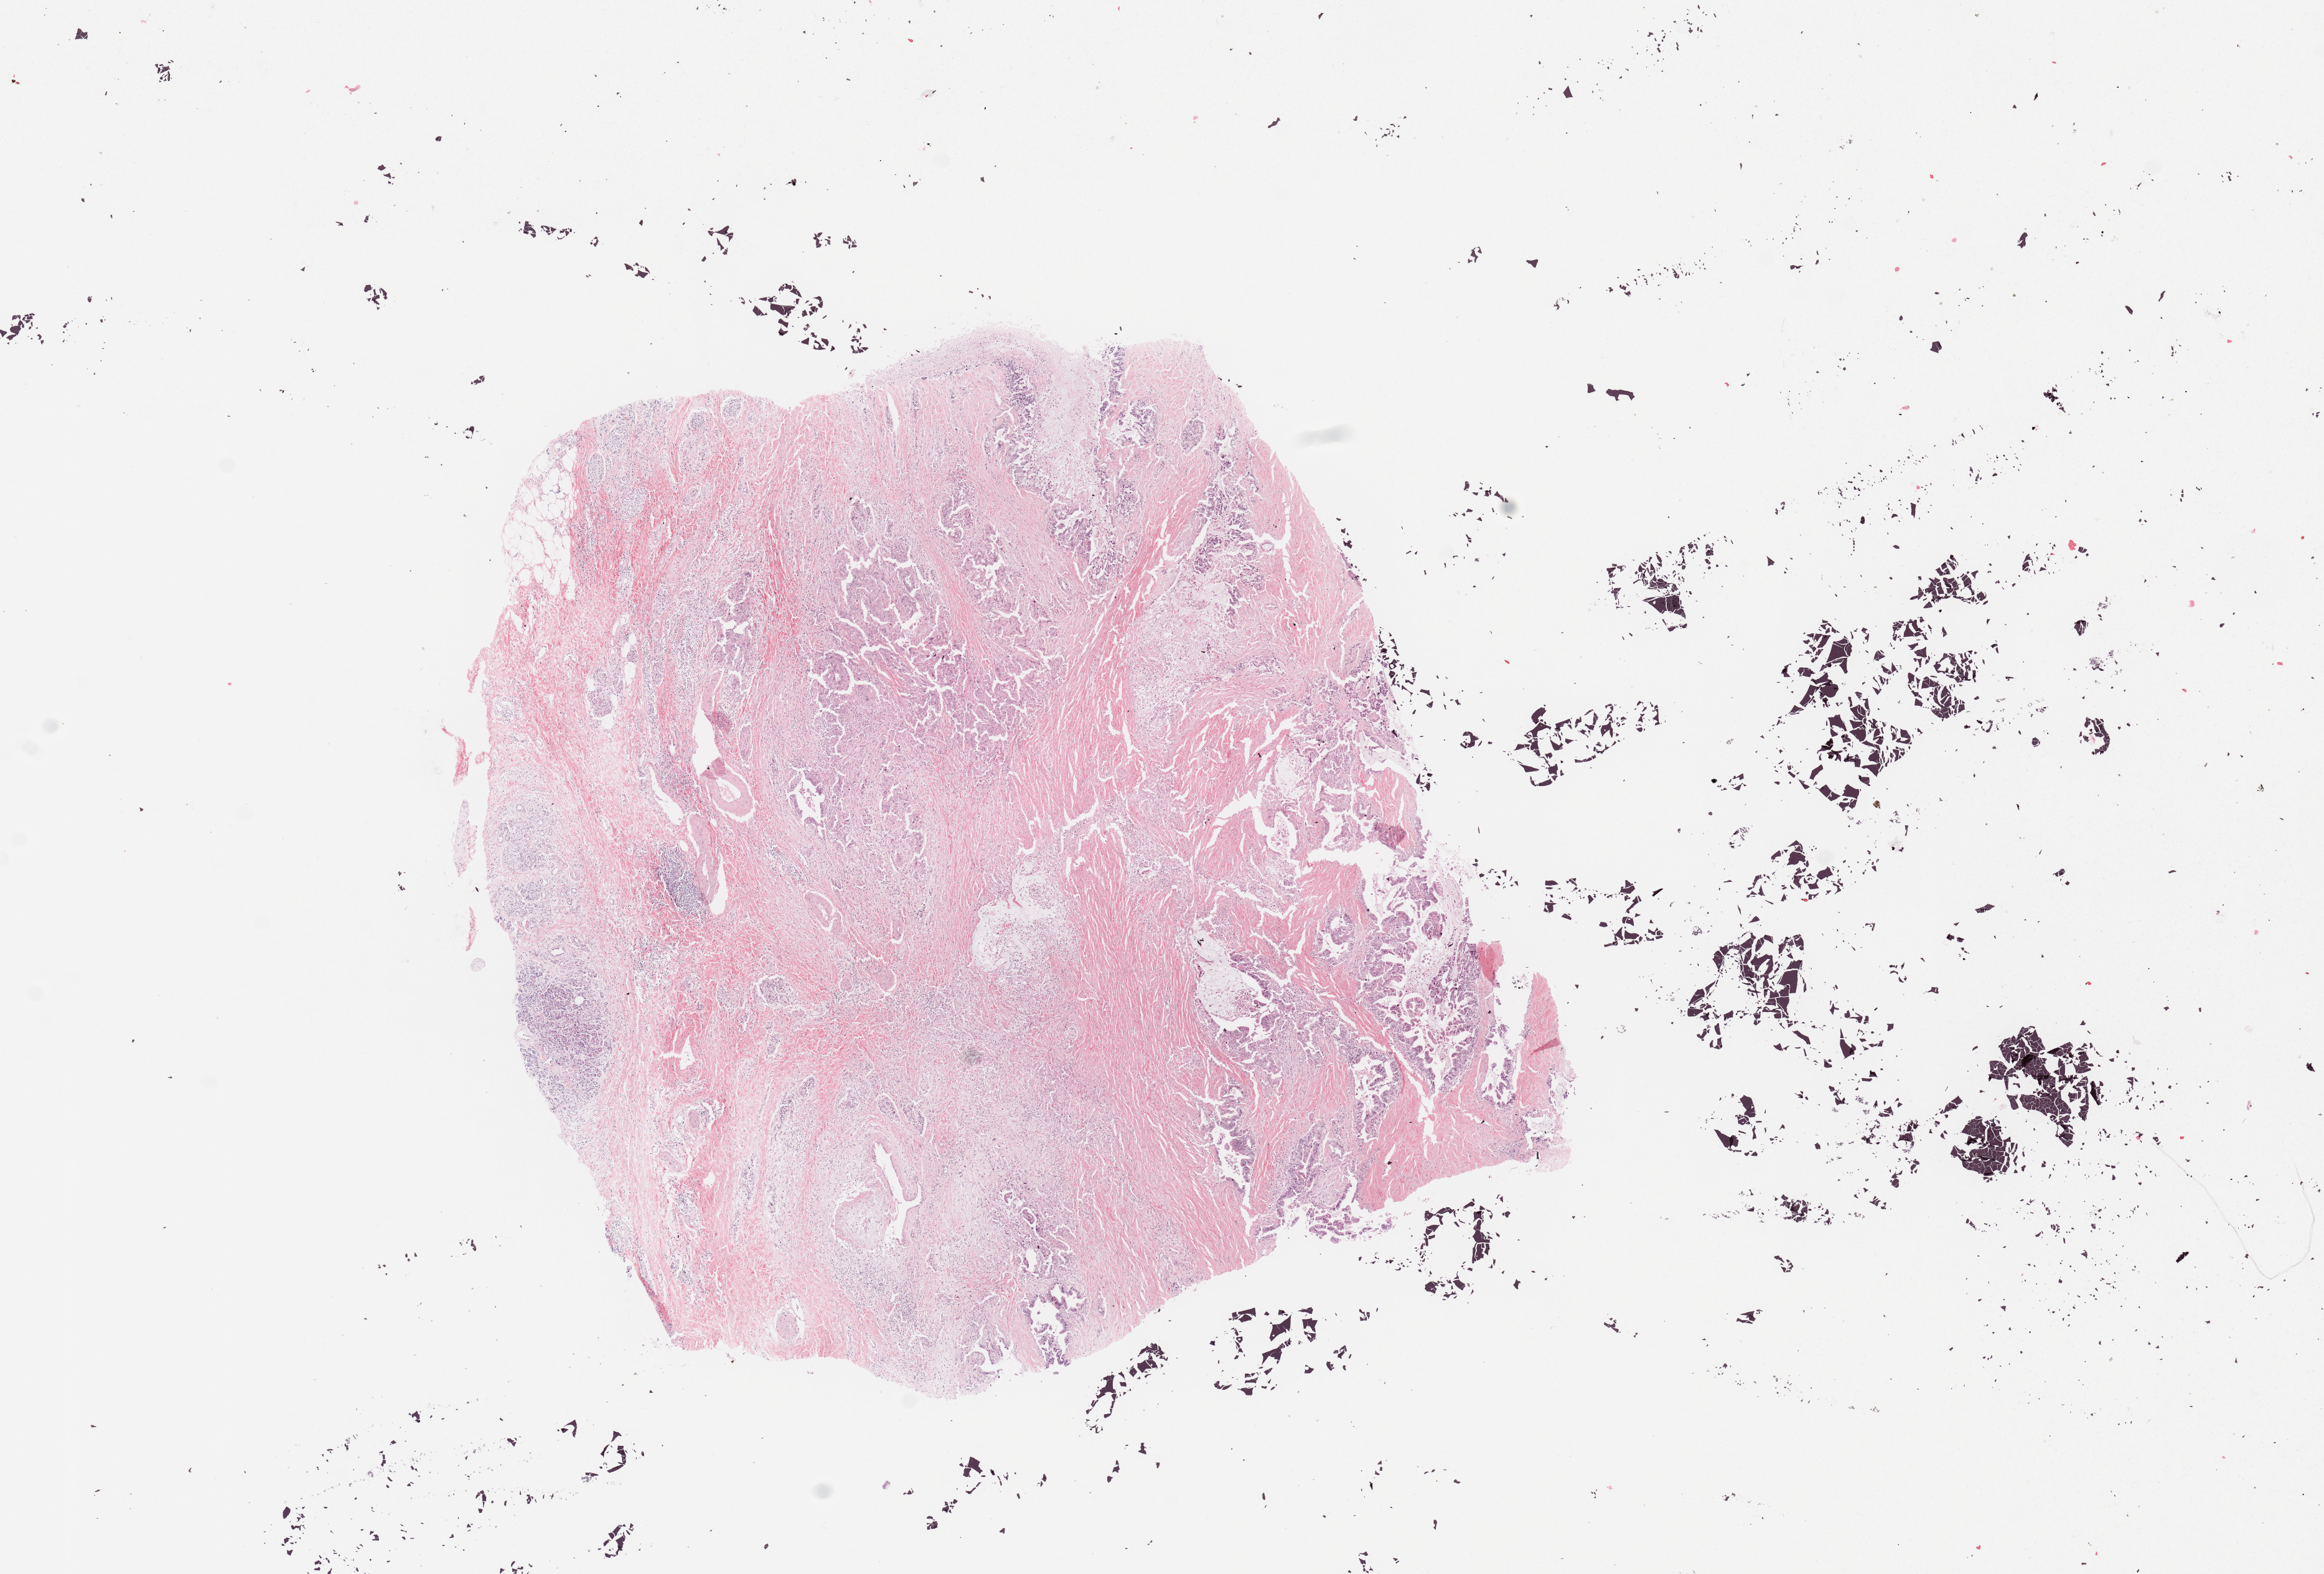
H&E whole-slide image — shown as a low-resolution overview of the whole scanned area (about 14.8 x 10.0 mm). Tumour tissue sample, sampled site: pancreas. Female, 61 y/o. Histologic grade: G2 (moderately differentiated). Composition of this section per pathologist review: tumour nuclei 40%, necrosis 5%.
Diagnosis: Infiltrating duct carcinoma, NOS. AJCC pathologic stage: IB.